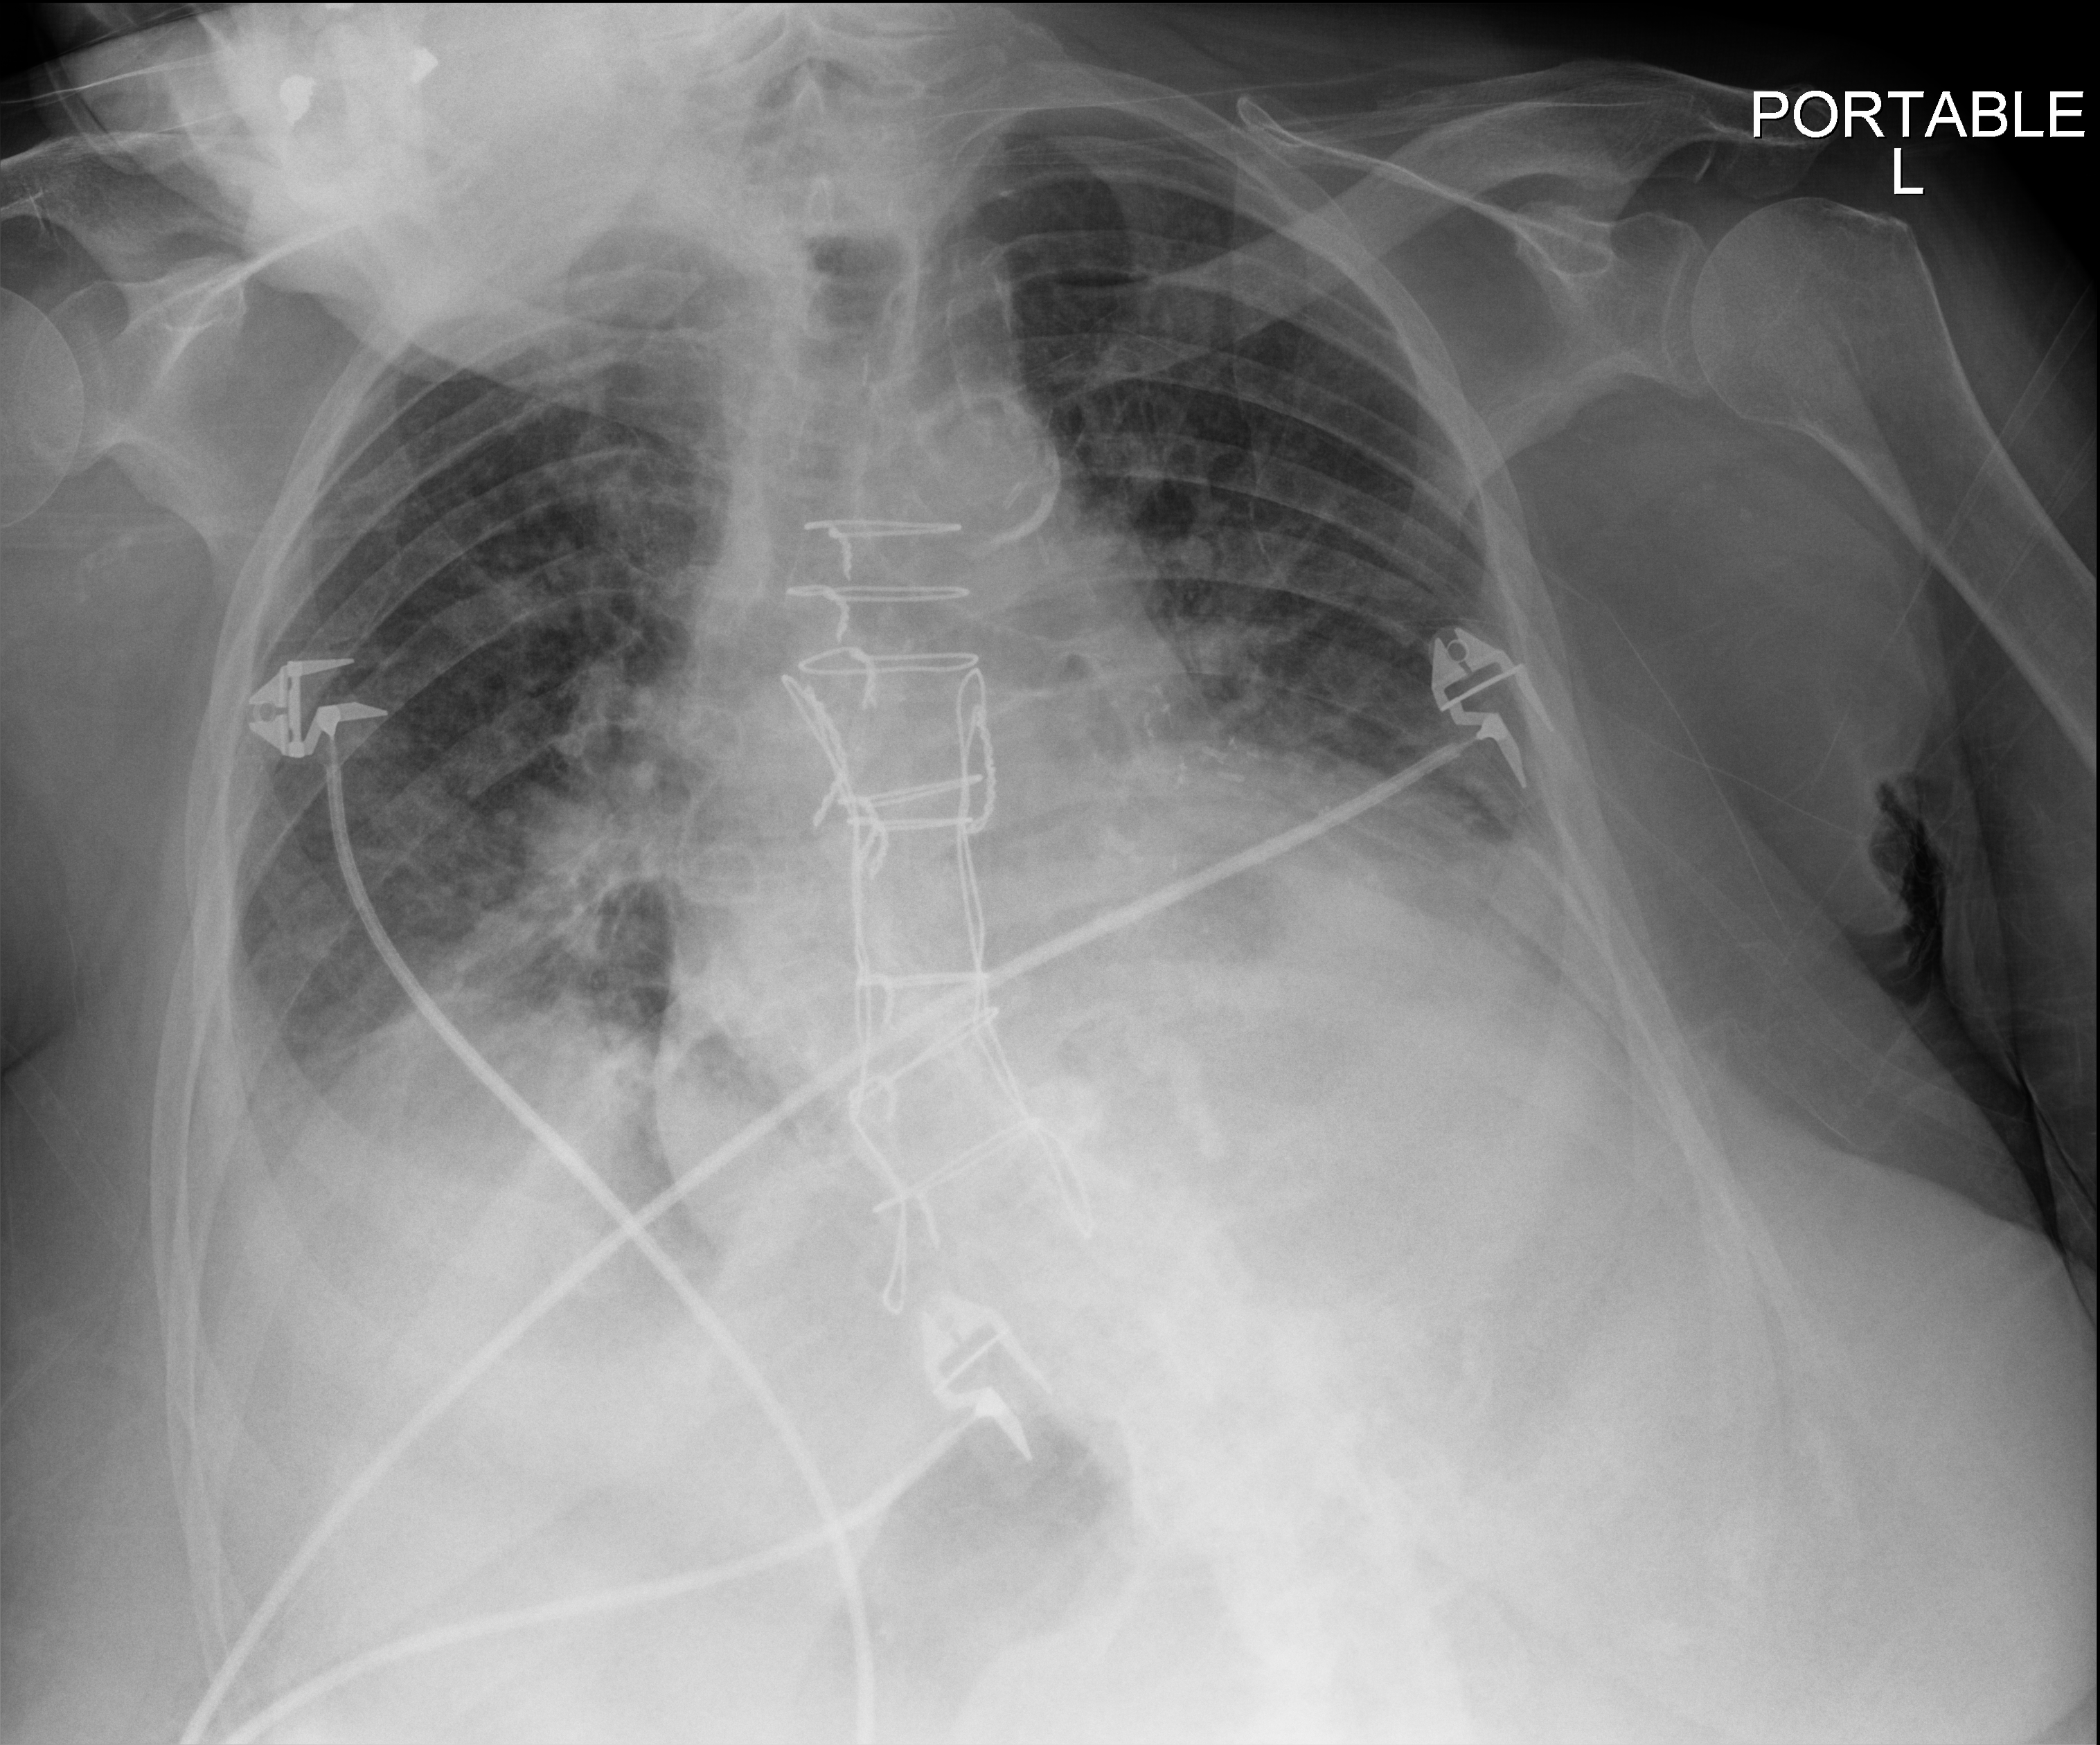
Chest radiograph (digital radiography). Patient hospitalised with COVID-19; female, aged 75–90 years.
Admission-level facts for this patient (not findings on this image; timing relative to this image not recorded):
- mechanically ventilated during this hospital stay: no